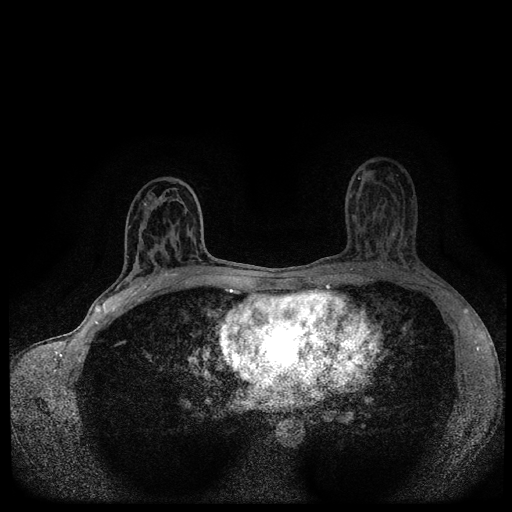
Breast MRI (dynamic contrast-enhanced, multi-phase), one axial slice; slice 55 of 116 in the series (ordered by position); dynamic contrast-enhanced series, time point 2 of 5 at this slice position (early post-contrast); 1.5 T; TE 2.7 ms, TR 5.4 ms; 2 mm slice thickness; 512 × 512 image matrix. Patient: female, 43 years.
Annotated regions visible in this slice (semi-automatically segmented with operator editing):
- breast lesion (labelled 'tumour' in the annotation; benign lesions carry a separate 'benign' label): box from (x=159, y=196) to (x=163, y=200) px